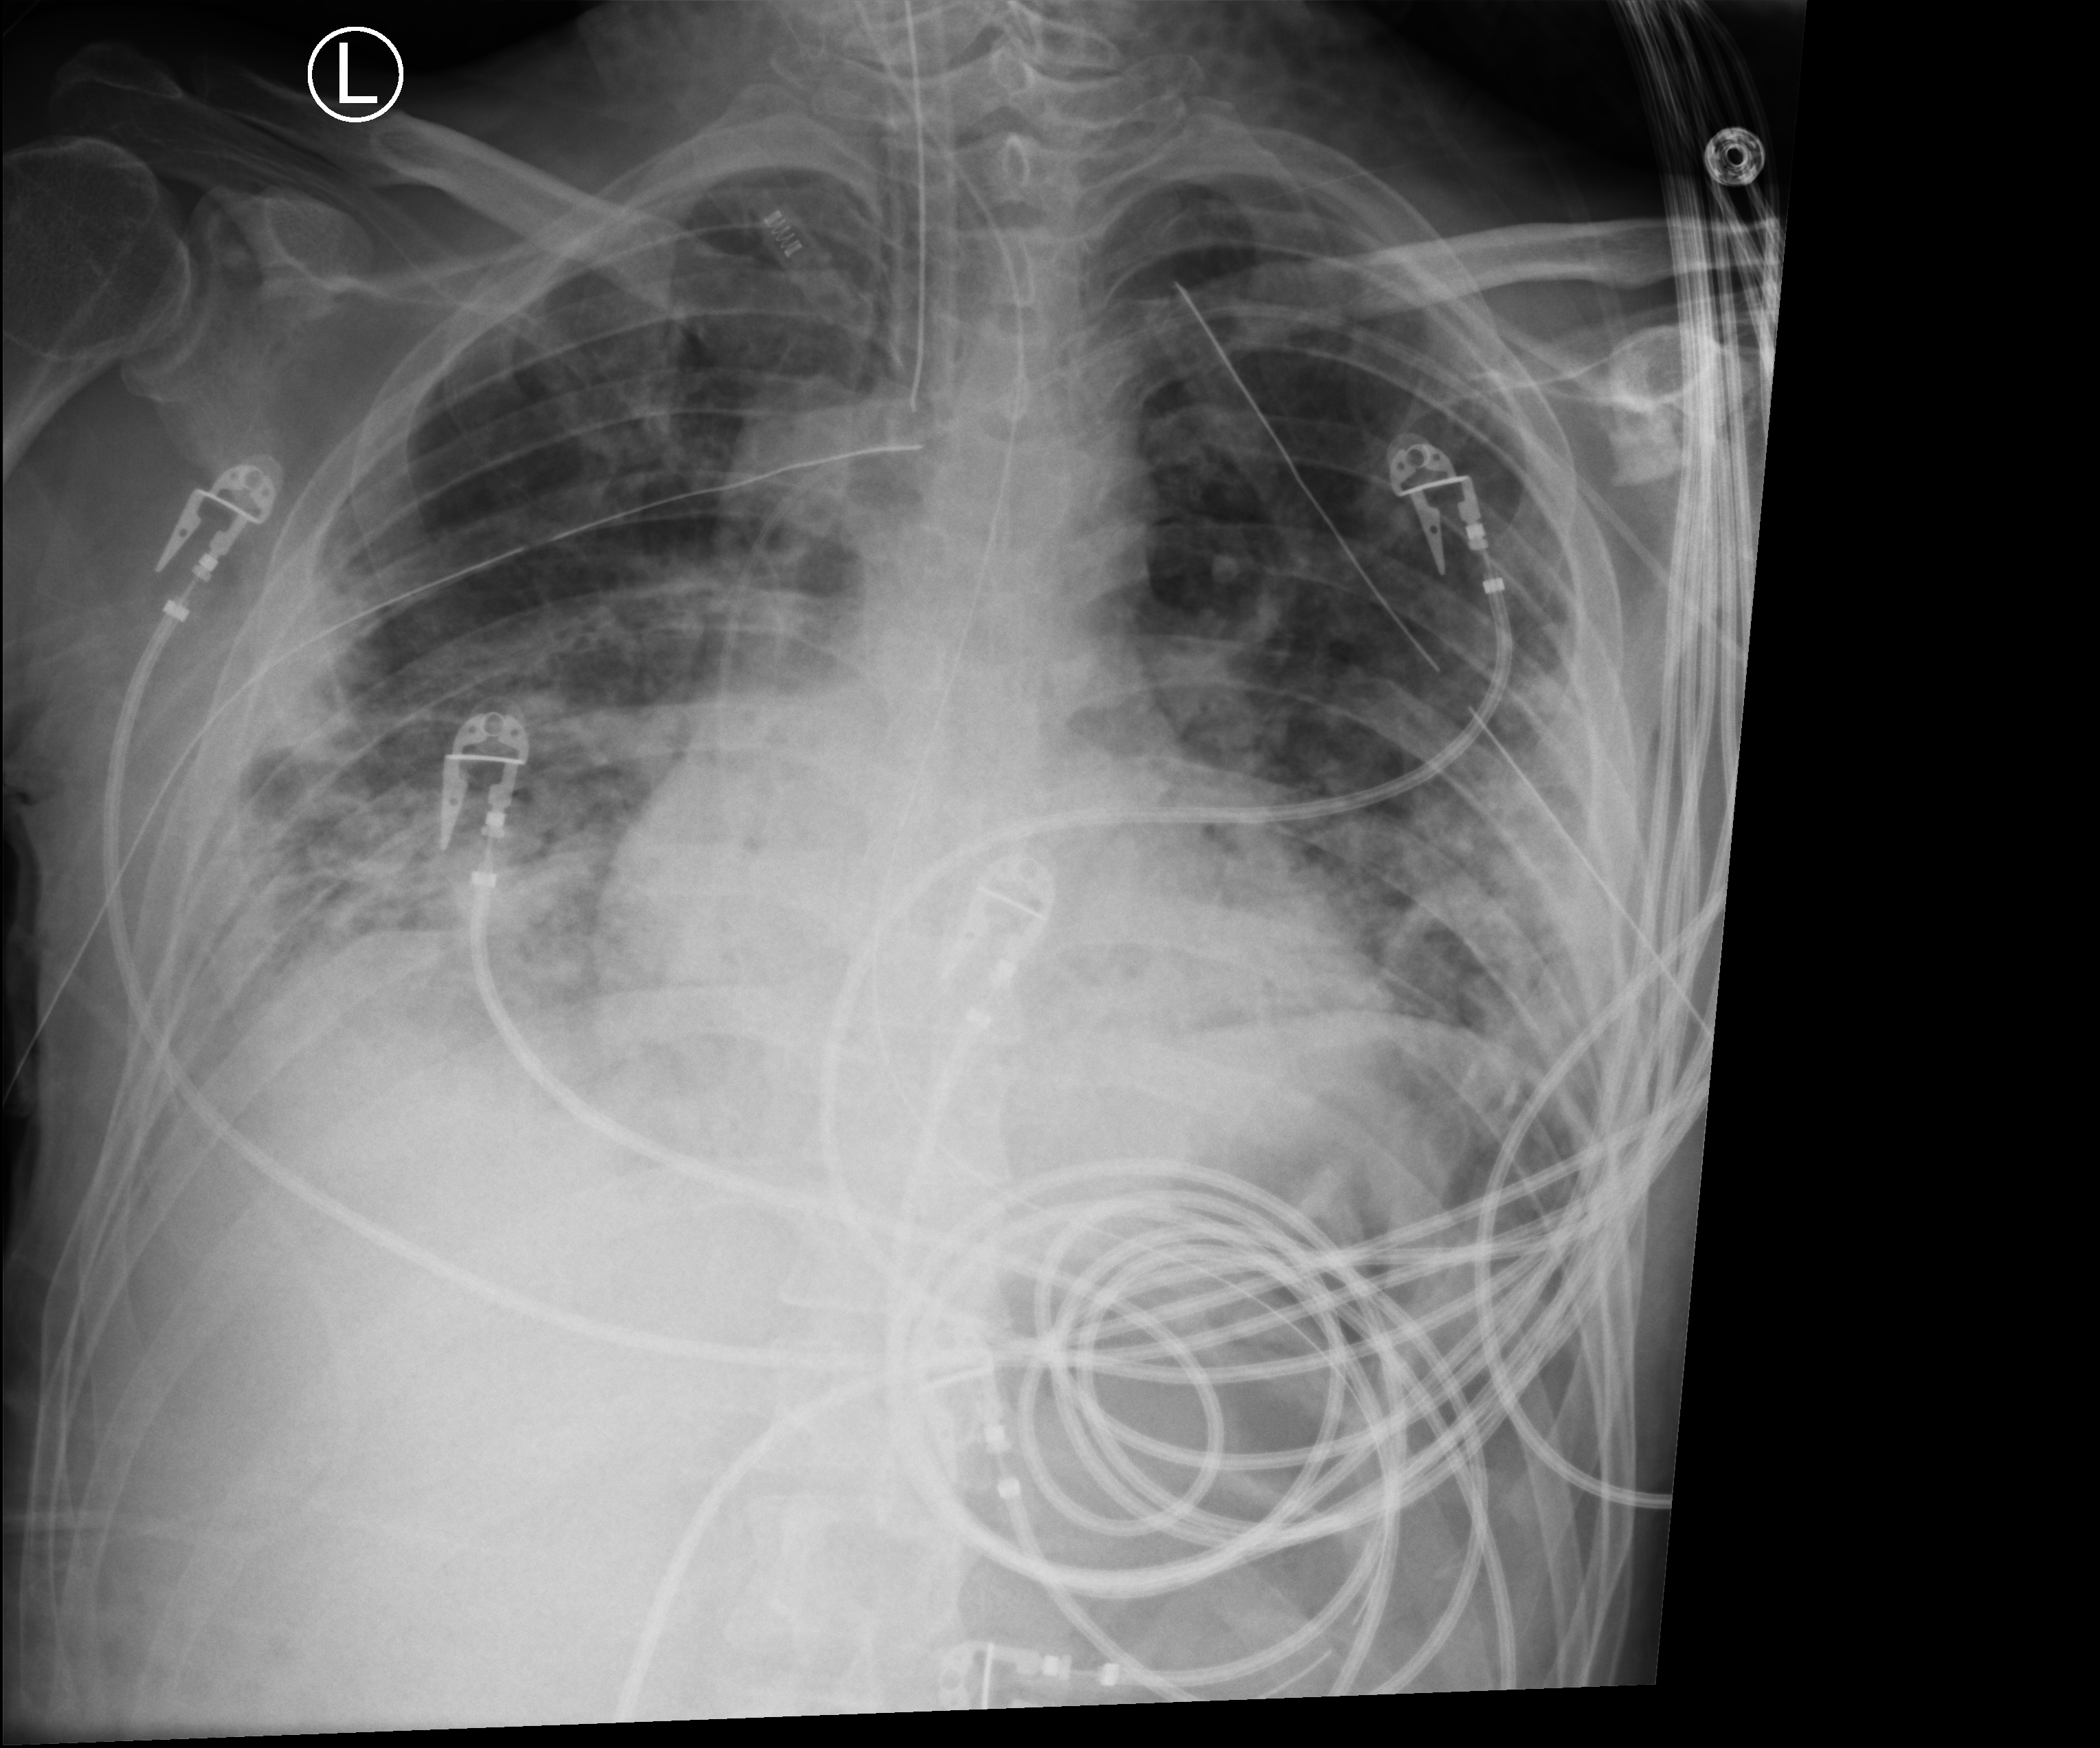
Portable chest radiograph, anteroposterior (AP) projection. Male patient hospitalised with COVID-19, age 18–59 years.
Admission-level facts for this patient (not findings on this image; timing relative to this image not recorded): length of hospital stay: 96 days.